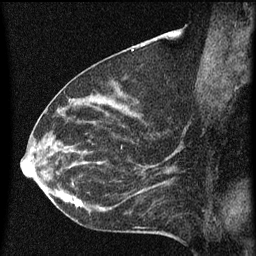
Breast MRI (dynamic contrast-enhanced), one sagittal slice. Slice 29 of 60 in the series (ordered by position). Dynamic contrast-enhanced series, image 2 of 3 at this slice position (ordered by acquisition). 1.5 T. TE 4.2 ms, TR 8 ms. 256 × 256 image matrix, field of view 180 × 180 mm. Female patient, age 55 years.
Structures marked on this image (semi-automatic segmentation, software-assisted and operator-edited):
- analysis volume of interest (the breast-tissue region the enhancement analysis was run in; not a lesion): bounding box [x1, y1, x2, y2] px = [51, 156, 145, 217]
- tumour enhancement mask (voxels above the 70 % enhancement threshold inside the analysis volume of interest): [51, 162, 145, 209]